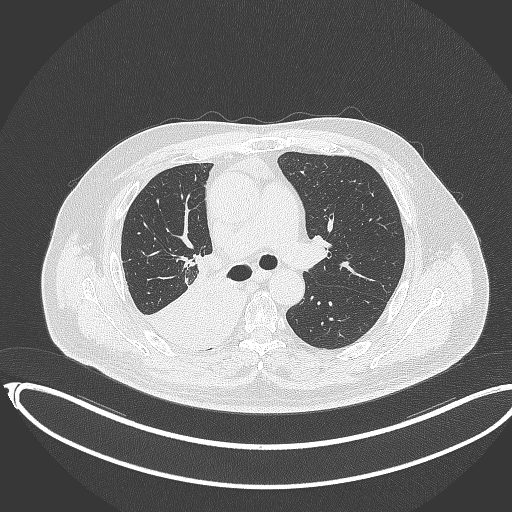
Chest CT, one axial slice; position 225 of 403 along the scan axis; 120 kVp; lung window (W 1500 / L -600 HU); 1 mm slice thickness; 512 × 512 image matrix, field of view 436 × 436 mm. Patient: male, 68 years. Case-level facts recorded for this patient, not image findings: clinical TNM (as recorded): T2a N0 M0.
Structures marked on this image (bounding box drawn by a radiologist):
- lung tumour (recorded histology: adenocarcinoma): bounding box (x1, y1, x2, y2) in pixels: (141, 264, 241, 351)